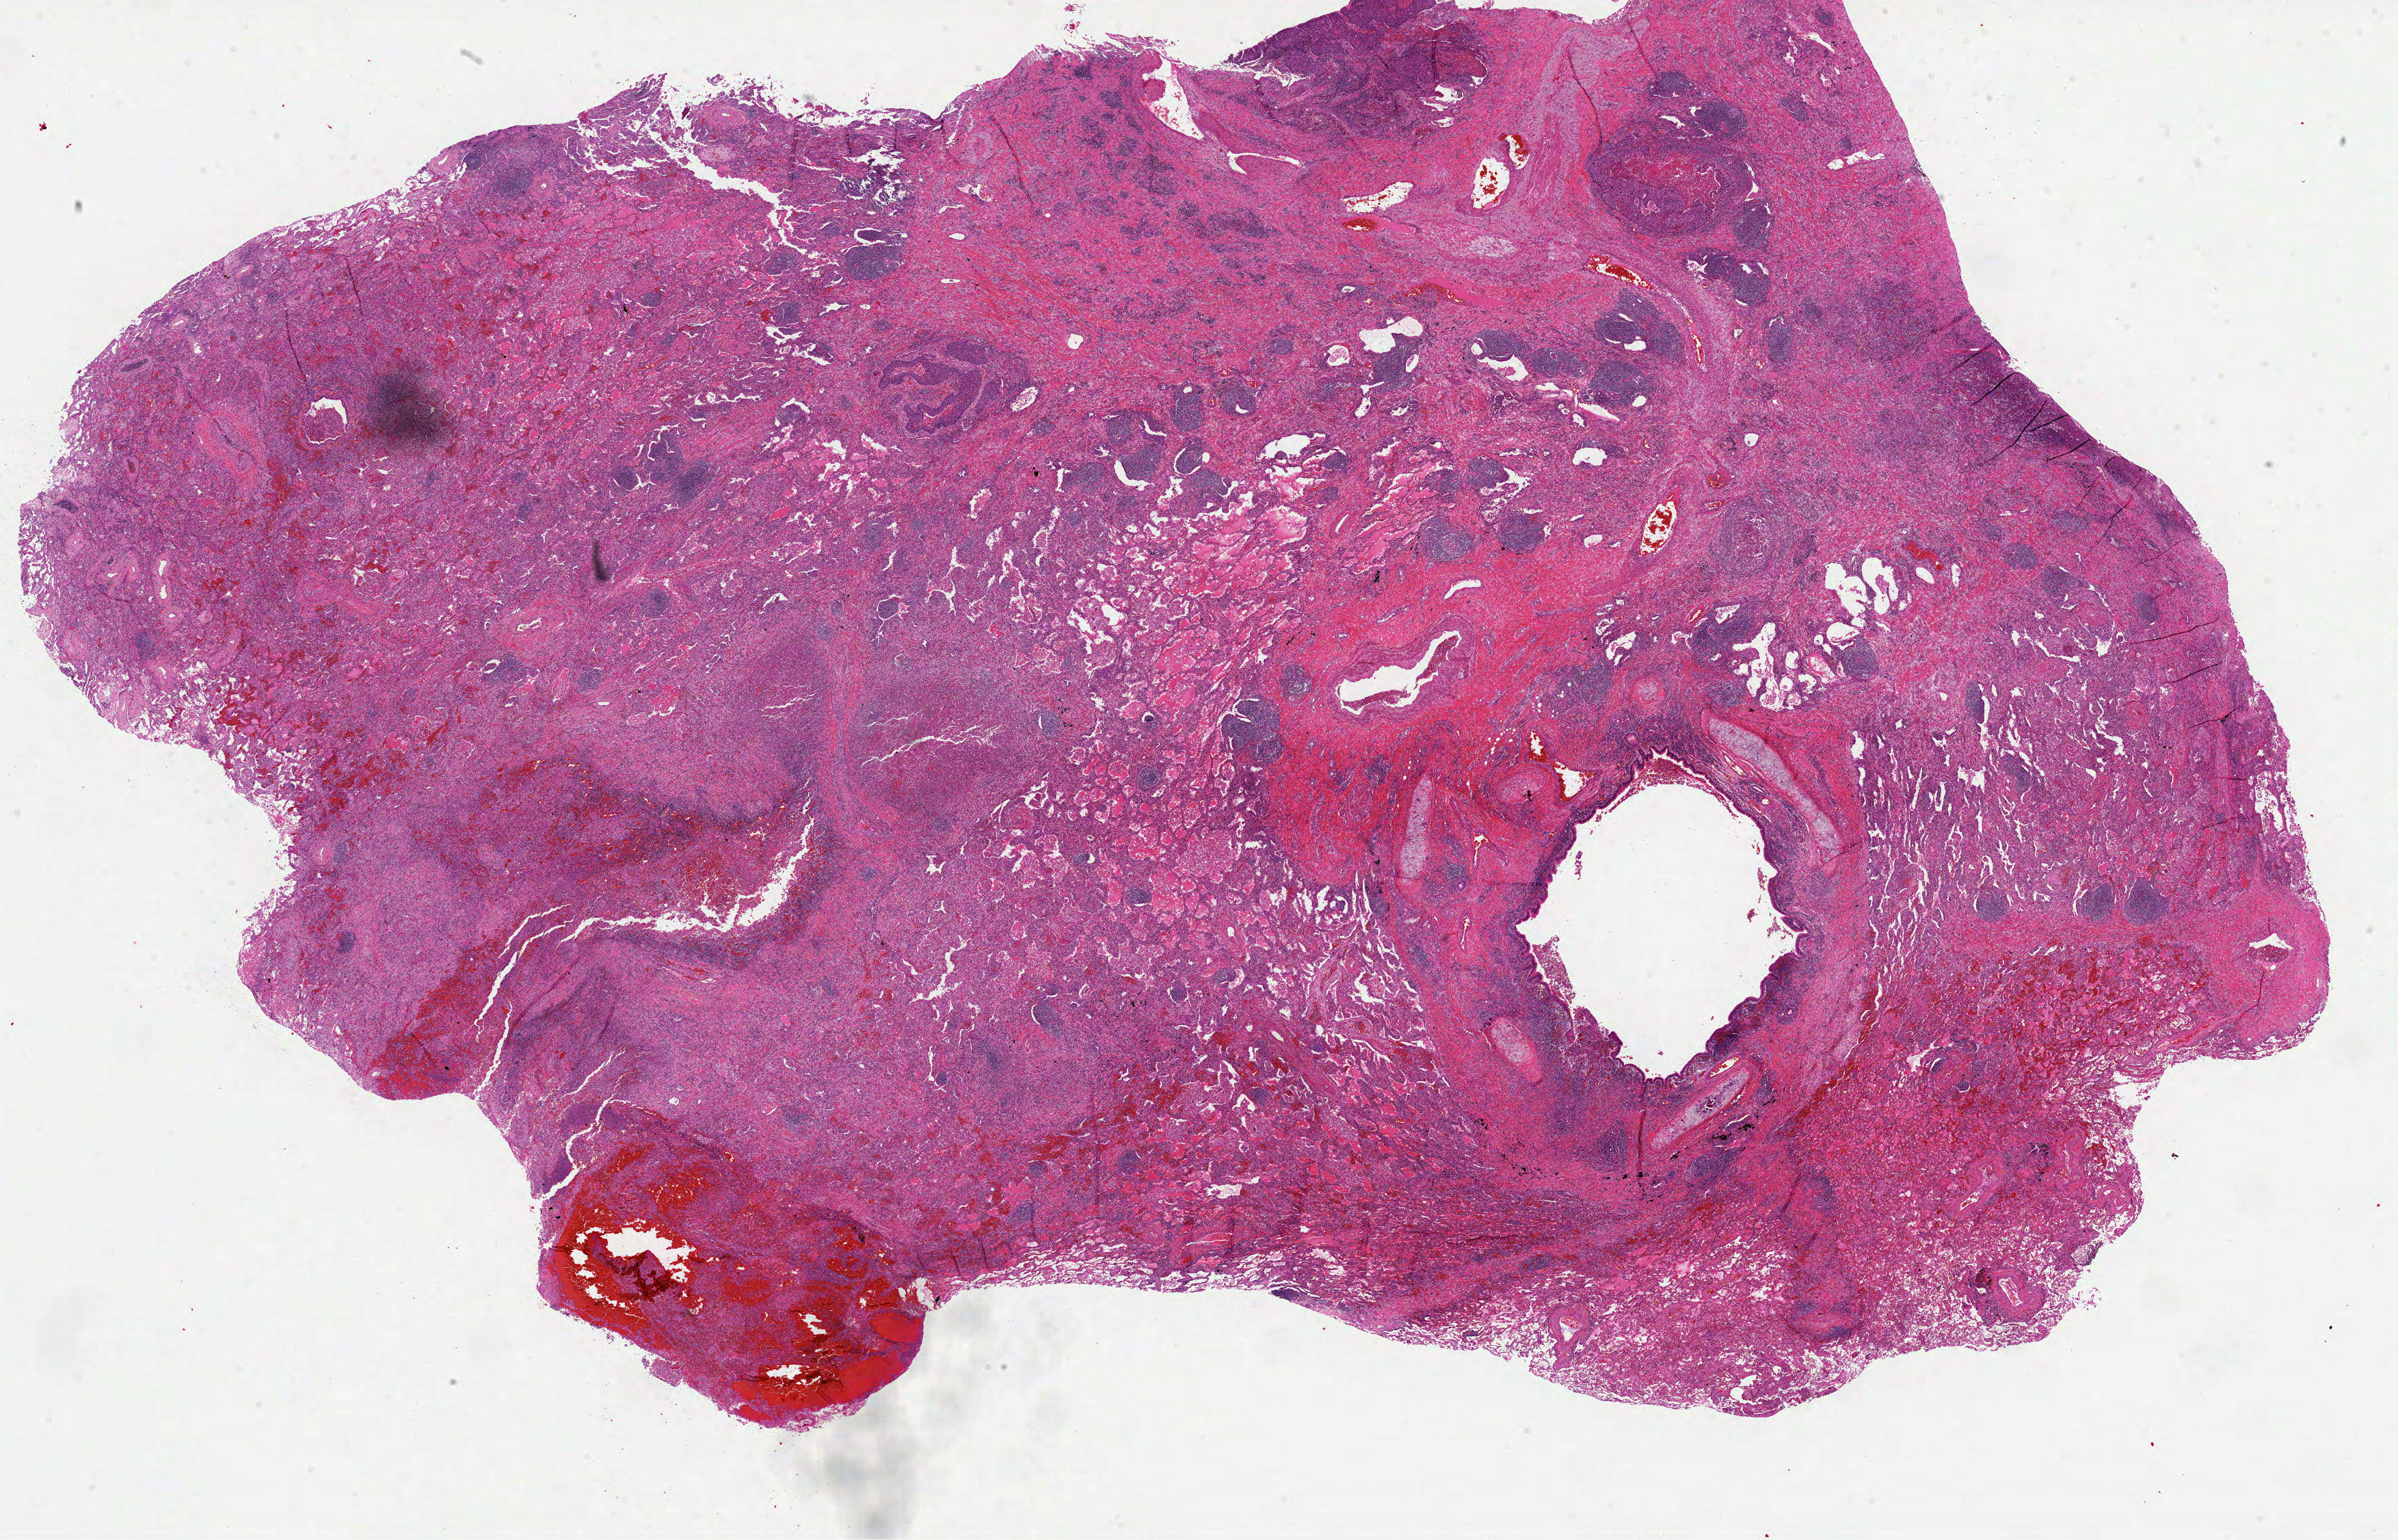
Digitized H&E tissue section (whole slide), whole scanned area (about 28.3 x 18.2 mm) shown as a low-resolution overview, formalin-fixed paraffin-embedded (FFPE) diagnostic section, lung, primary tumour sample. Male patient; age at initial diagnosis 73 years.
• histologic diagnosis: Squamous cell carcinoma, NOS (lower lobe, lung)
• AJCC pathologic stage: IA